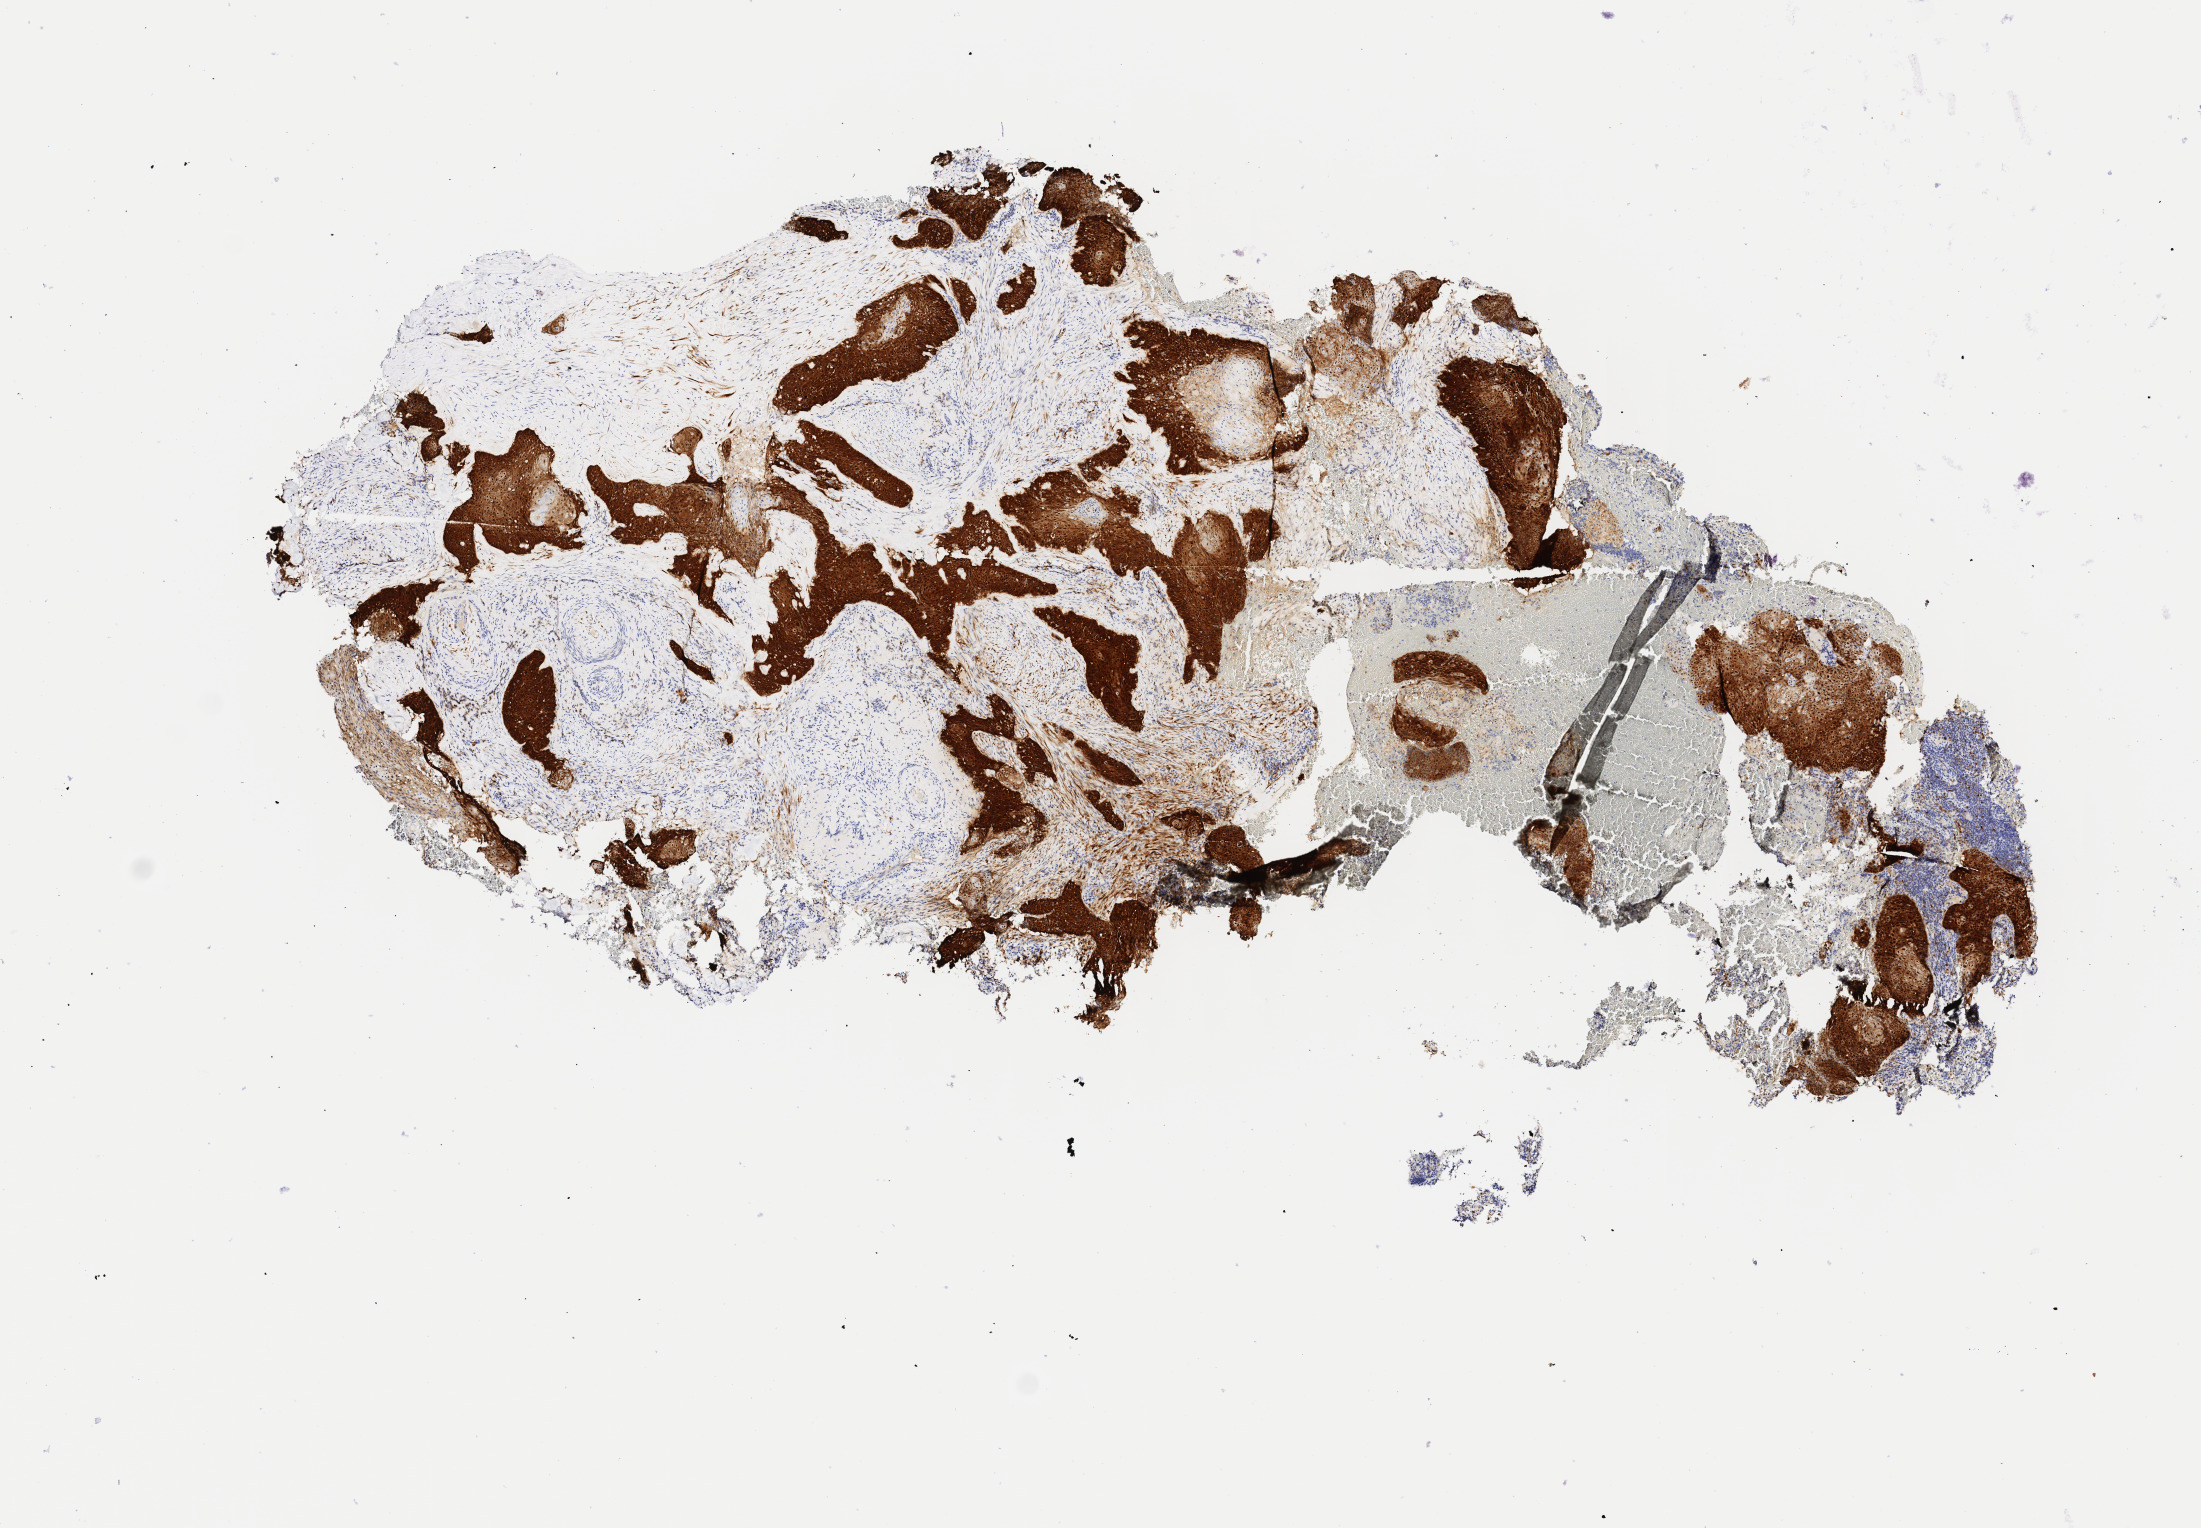
IHC for p16 (p16INK4a), whole-slide image, shown as a low-resolution overview of the whole scanned area (about 8.8 x 6.1 mm). Specimen: tumor tissue. Anatomic site: cervix. Patient: female, age 54 years.
• diagnosis: Squamous cell carcinoma, keratinizing, NOS